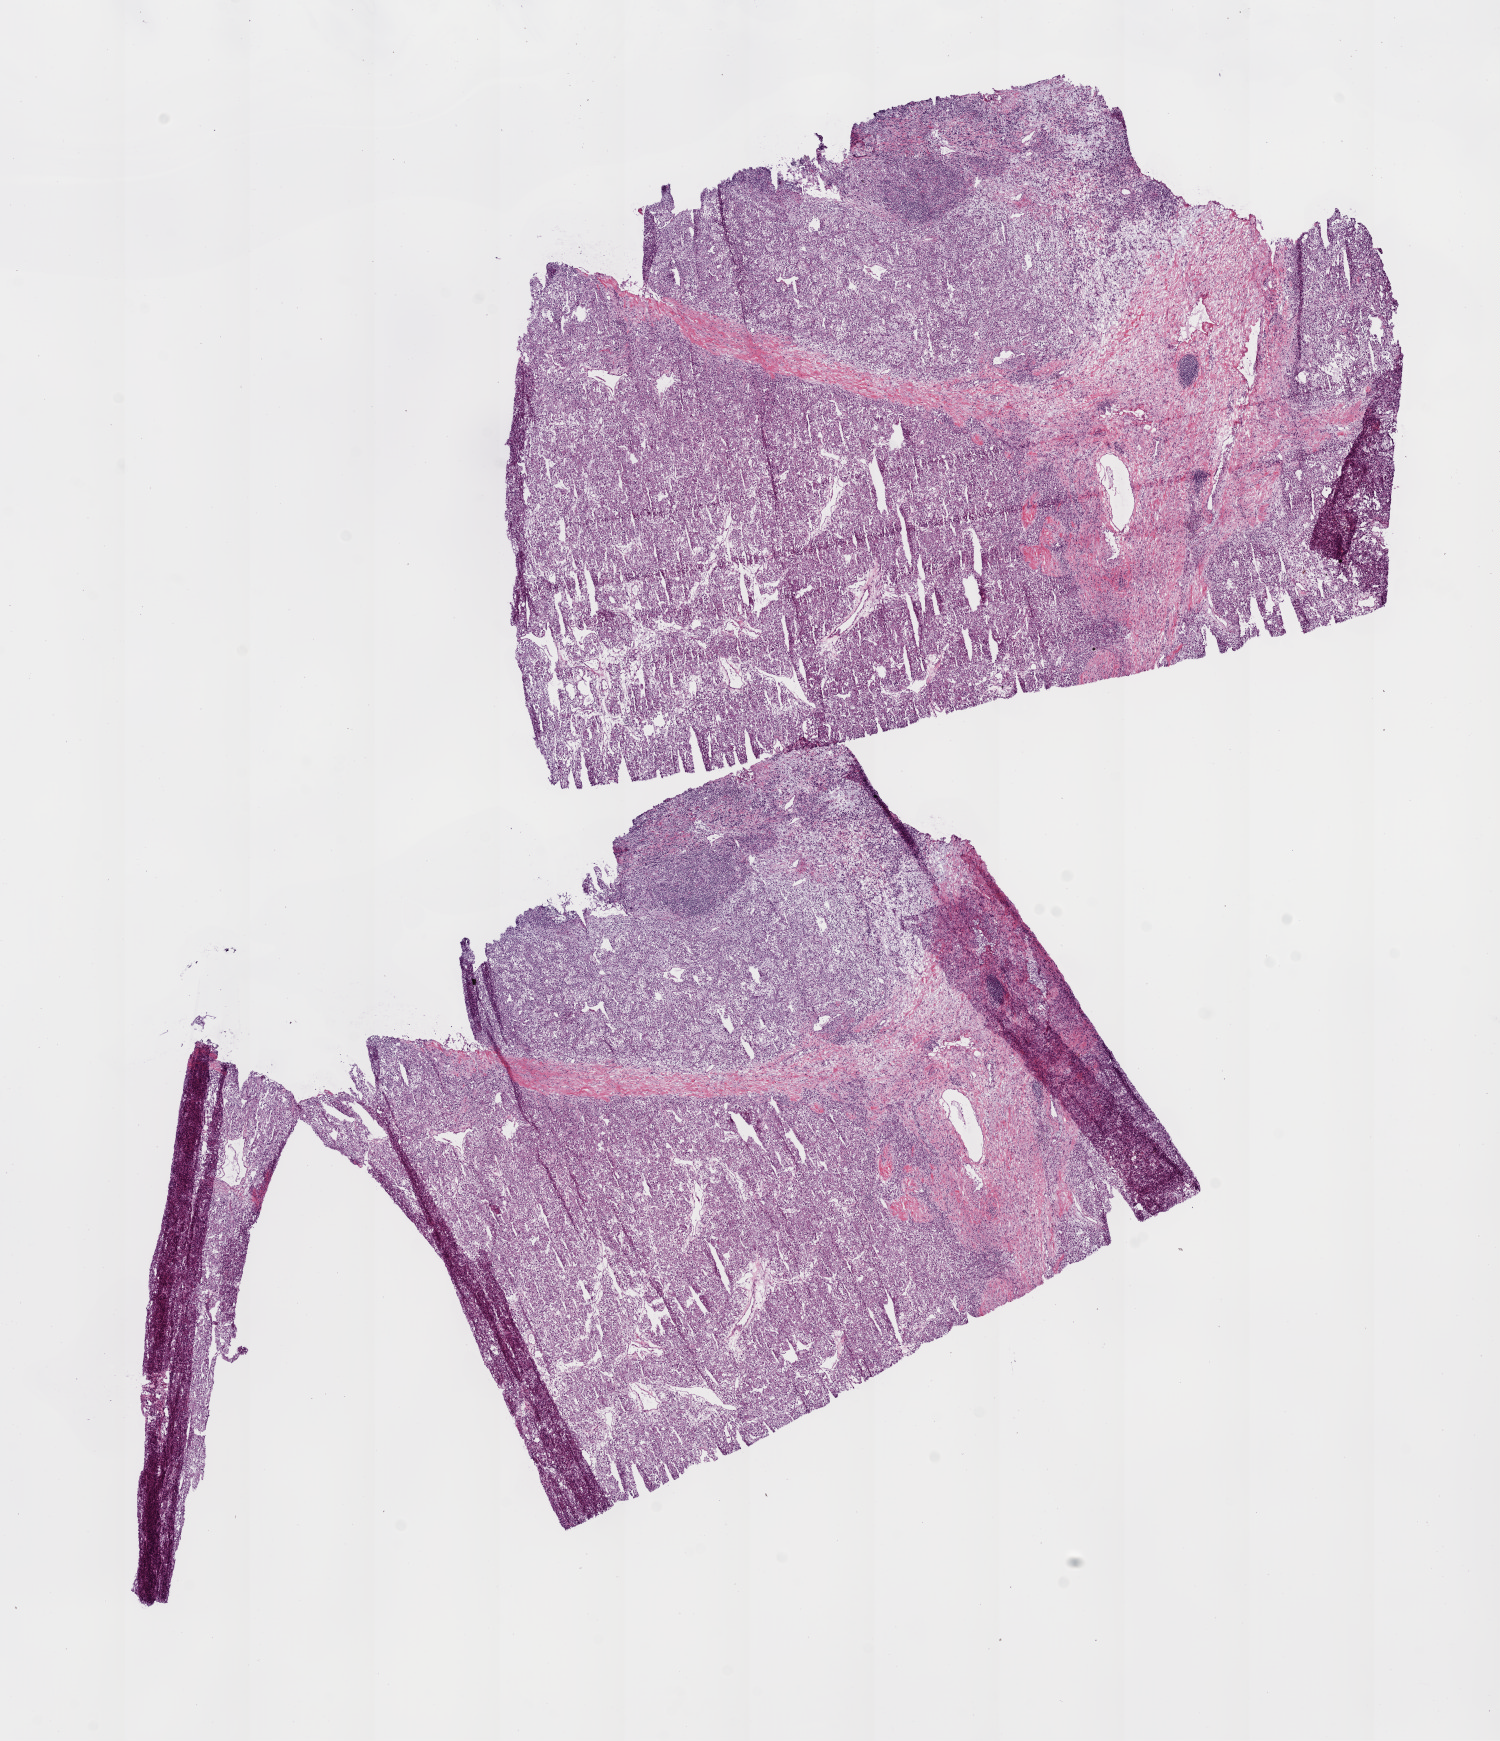
Digitized H&E-stained tissue section (whole slide), shown as a low-resolution overview of the whole scanned area (about 12.0 x 14.0 mm, from a 20x scan); frozen section from the bottom of the tissue portion; primary tumour sample from the kidney. Male patient; age at initial diagnosis 51 years. Histologic grade: G3 (poorly differentiated). Pathologist review of this section (percent, as recorded): tumour cells 85%, tumour nuclei 80%, normal cells 0%, stromal cells 15%, necrosis 0%. Infiltration values recorded for this section: lymphocyte infiltration 10%, monocyte infiltration 3%, neutrophil infiltration 0%.
Laterality: right. AJCC pathologic stage: IV. Pathologic diagnosis: Clear cell adenocarcinoma, NOS.